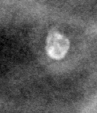
Cropped region of a digitized screen-film mammogram centred on a radiologist-marked abnormality; right breast; MLO view; BI-RADS breast density category 3 (scale 1–4).
- Finding: calcifications, morphology lucent center; BI-RADS assessment category 2; benign without callback (not worked up further).